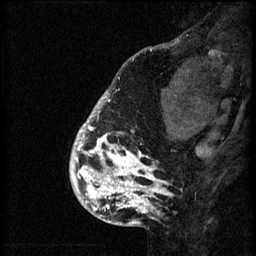
Breast MRI (dynamic contrast-enhanced), one sagittal slice; position 15 of 60 along the scan axis; 3 images stored at this slice position (order not interpretable as contrast timing); 1.5 T; TE 4.2 ms, TR 8.2 ms; 2 mm slice thickness; 256 × 256 image matrix, field of view 180 × 180 mm. Female patient, age 41 years.
Annotated regions visible in this slice (semi-automatically segmented with operator editing):
- analysis volume of interest (the breast-tissue region the enhancement analysis was run in; not a lesion): bounding box [x1, y1, x2, y2] px = [72, 108, 176, 205]
- tumour enhancement mask (voxels above the 70 % enhancement threshold inside the analysis volume of interest): [72, 108, 169, 205]